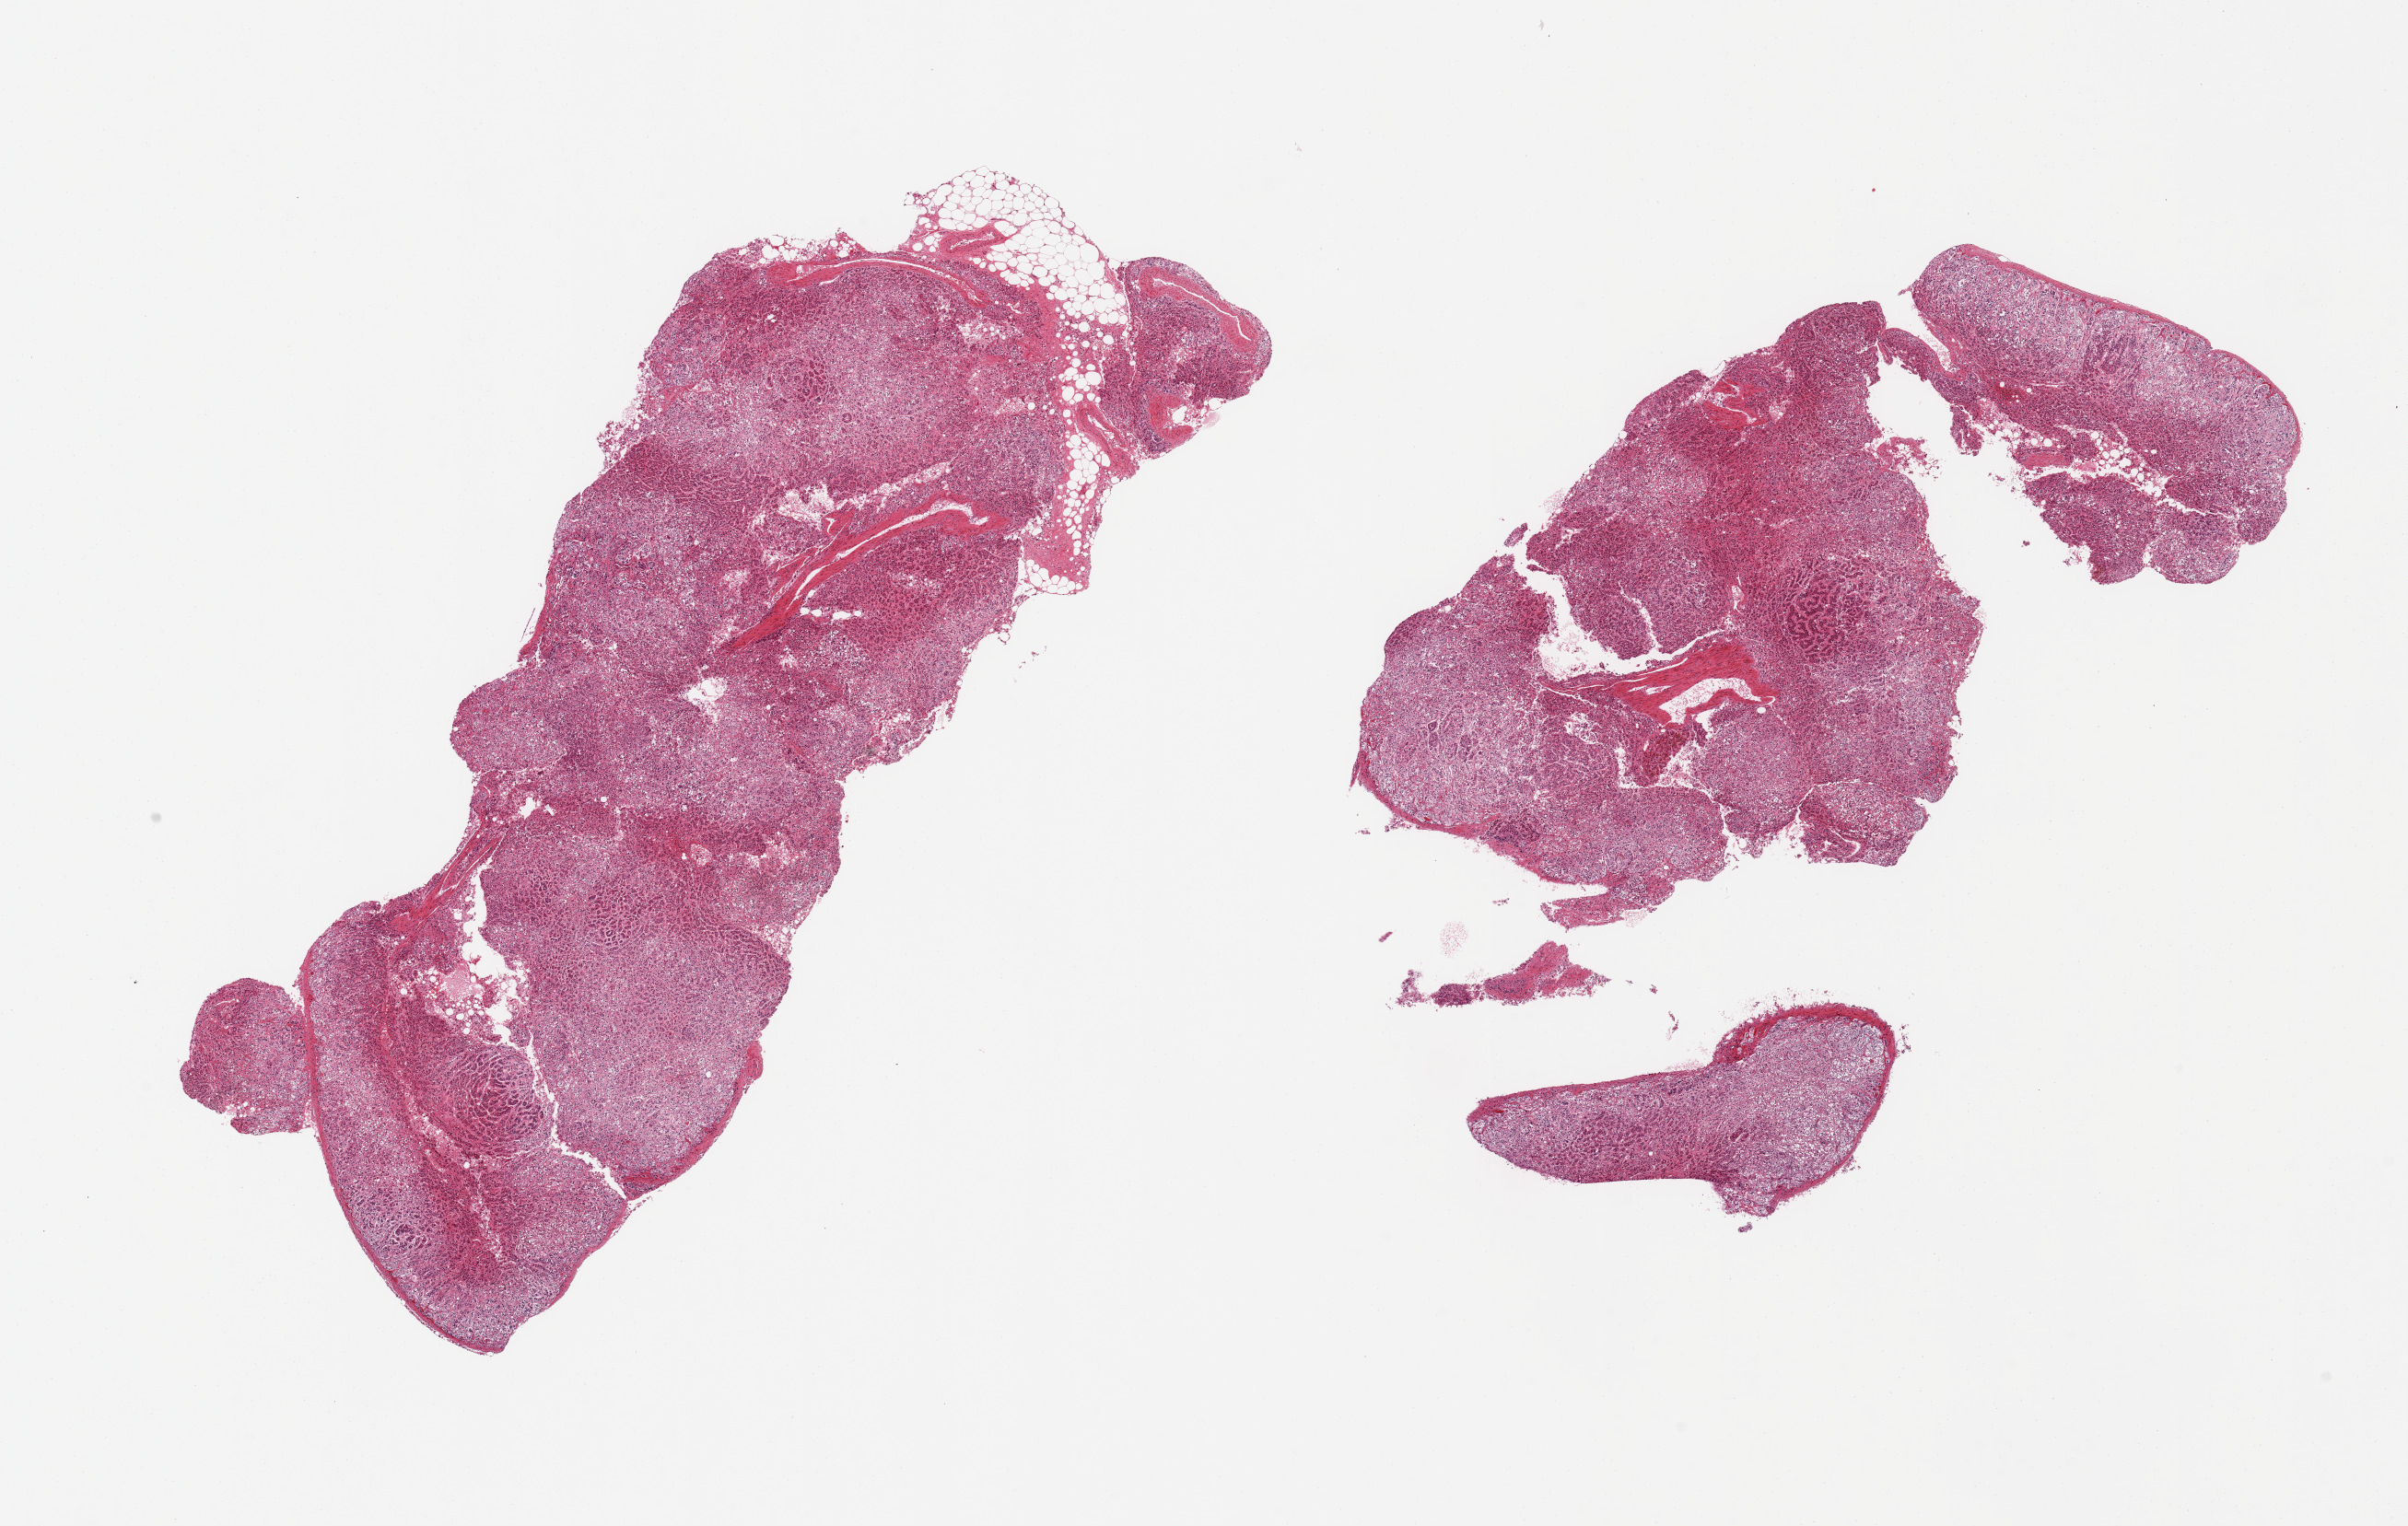
Digitized hematoxylin and eosin (H&E)-stained section, brightfield — a low-resolution overview of the entire scanned area, about 20.7 x 13.1 mm (from a 20x scan); PAXgene-fixed, paraffin-embedded tissue; section of adrenal gland (target tissue); tissue donor sample. Male donor.
Pathologist's review note for this sample: 2 pieces, cortex, advanced autolysis.